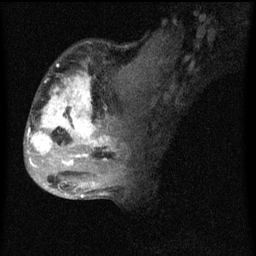
Breast MRI (dynamic contrast-enhanced), one sagittal slice; slice 28 of 60 in the series (ordered by position); dynamic contrast-enhanced series, image 2 of 4 at this slice position (ordered by acquisition); 1.5 T; TE 4.2 ms, TR 8 ms; 2 mm slice thickness; 256 × 256 image matrix, field of view 180 × 180 mm. Female patient, age 50 years.
Structures marked on this image (semi-automatic segmentation, software-assisted and operator-edited):
- analysis volume of interest (the breast-tissue region the enhancement analysis was run in; not a lesion): bounding box [x1, y1, x2, y2] px = [26, 44, 124, 177]
- tumour enhancement mask (voxels above the 70 % enhancement threshold inside the analysis volume of interest): [28, 74, 118, 167]